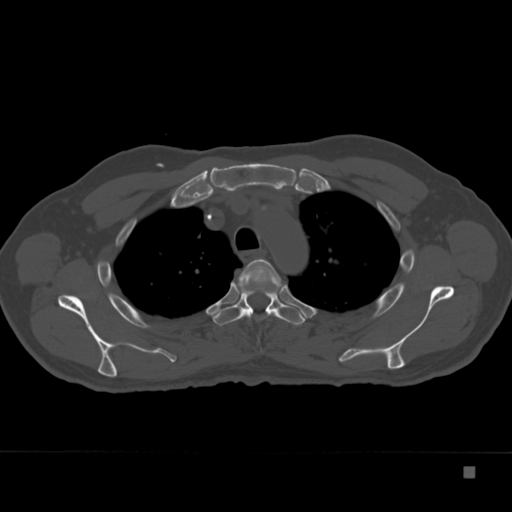
CT including the spine, one axial slice; slice 277 of 332 in the series (ordered by position); reconstruction kernel Br40s; 120 kVp; bone window (W 1800 / L 400 HU); 1.5 mm slice thickness; 512 × 512 image matrix, field of view 389 × 389 mm. Patient: male, 72 years. Case-level facts recorded for this patient, not image findings: primary cancer: skeletal.
Structures marked on this image (semi-automatic segmentation, software-assisted and operator-edited):
- T3 vertebra: box from (x=238, y=259) to (x=285, y=299) px
- T4 vertebra: (x=213, y=288)–(x=305, y=325)